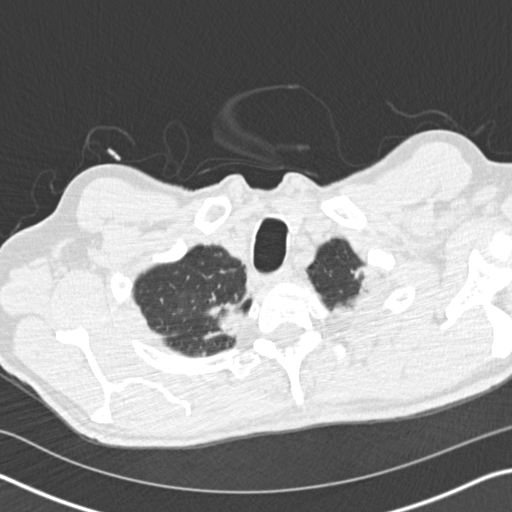
Low-dose screening chest CT, one axial slice; position 159 of 175 along the scan axis; reconstruction kernel B30f; 120 kVp; lung window (W 1500 / L -600 HU); 2 mm slice thickness; 512 × 512 image matrix, field of view 340 × 340 mm.
Outlined on this slice (outlined manually by an expert reader):
- lesion 1 (tumor, upper lobe of right lung): box from (x=207, y=301) to (x=247, y=337) px